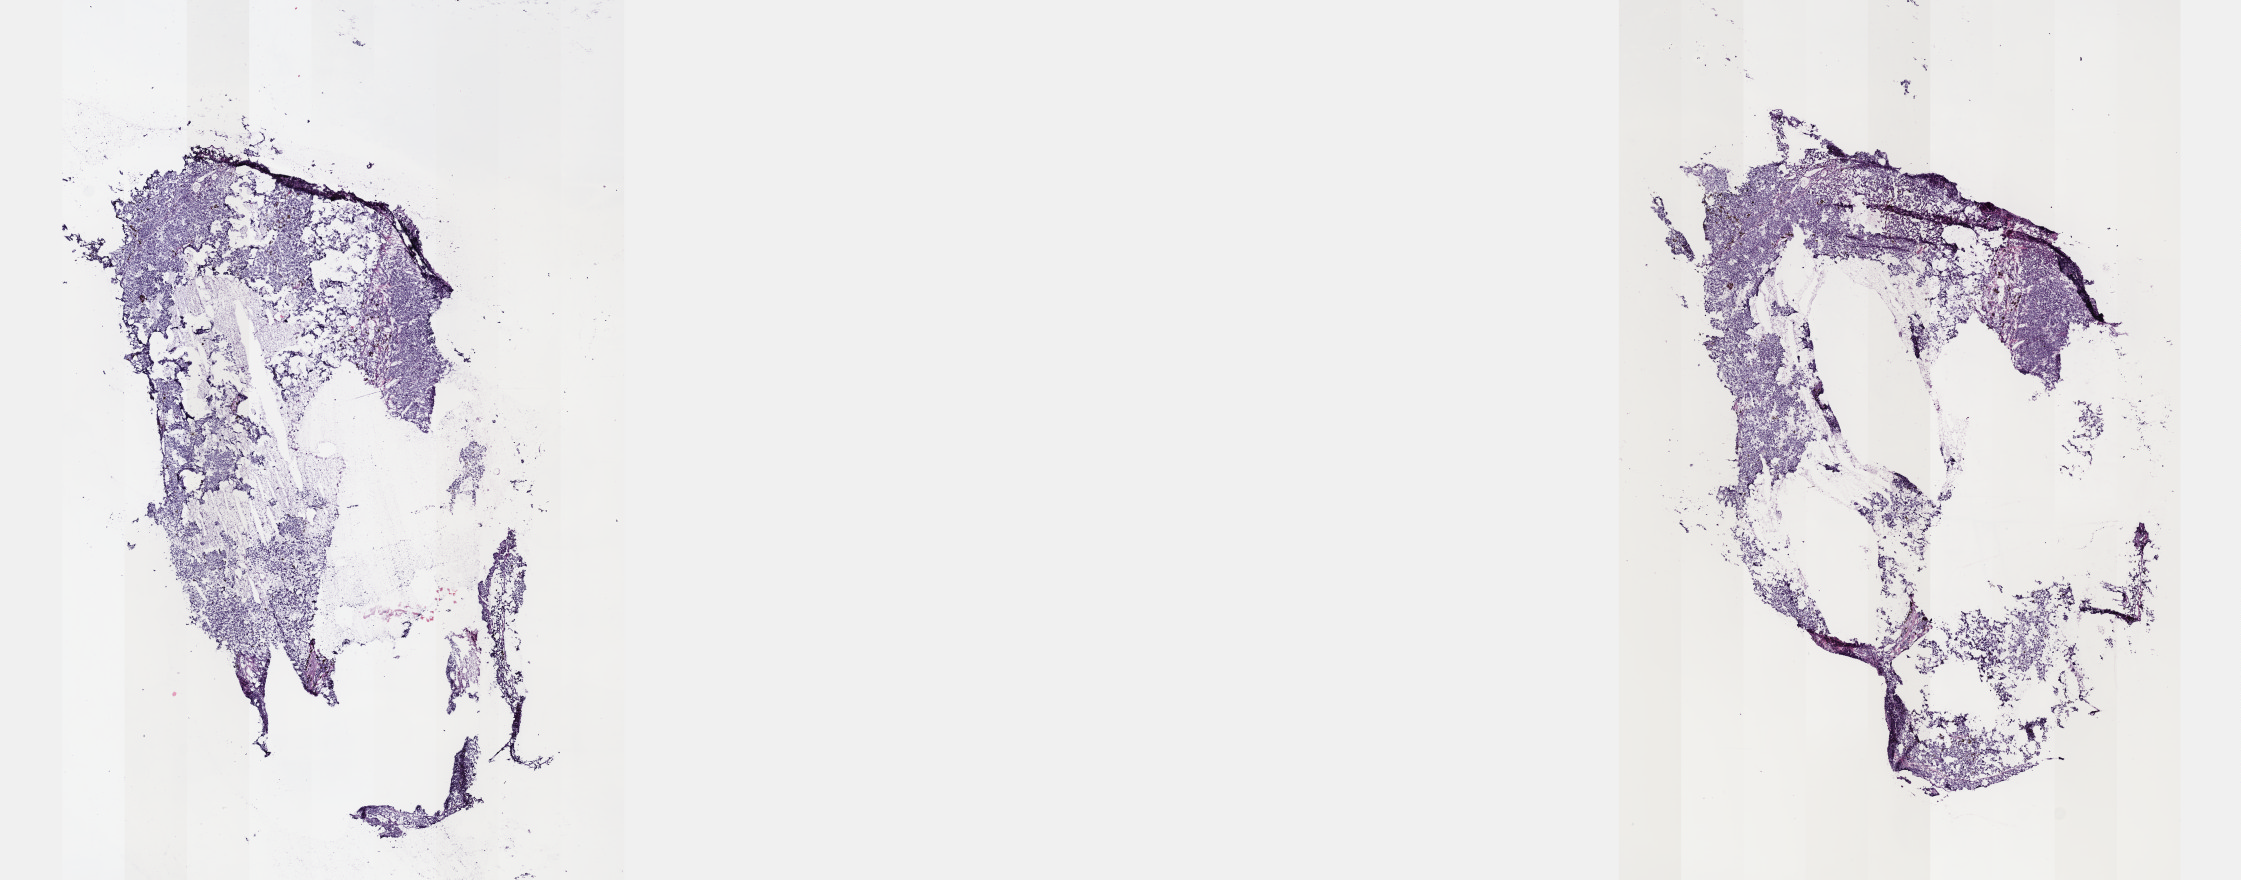
Digitized H&E tissue section (whole slide) — low-resolution overview of the scanned area, about 18.1 x 7.1 mm. Frozen section from the top of the tissue portion. Uvea, primary tumour sample. Female, age 83 years at initial diagnosis. Pathologist review of this section (percent, as recorded): tumour cells 90%, tumour nuclei 80%, normal cells 0%, stromal cells 0%, necrosis 10%. Infiltration values recorded for this section: lymphocyte infiltration 2%, monocyte infiltration 0%, neutrophil infiltration 0%.
* AJCC pathologic stage: IIIC
* TNM: T4d N0 M0
* histologic diagnosis: Epithelioid cell melanoma (ciliary body)
* laterality: left